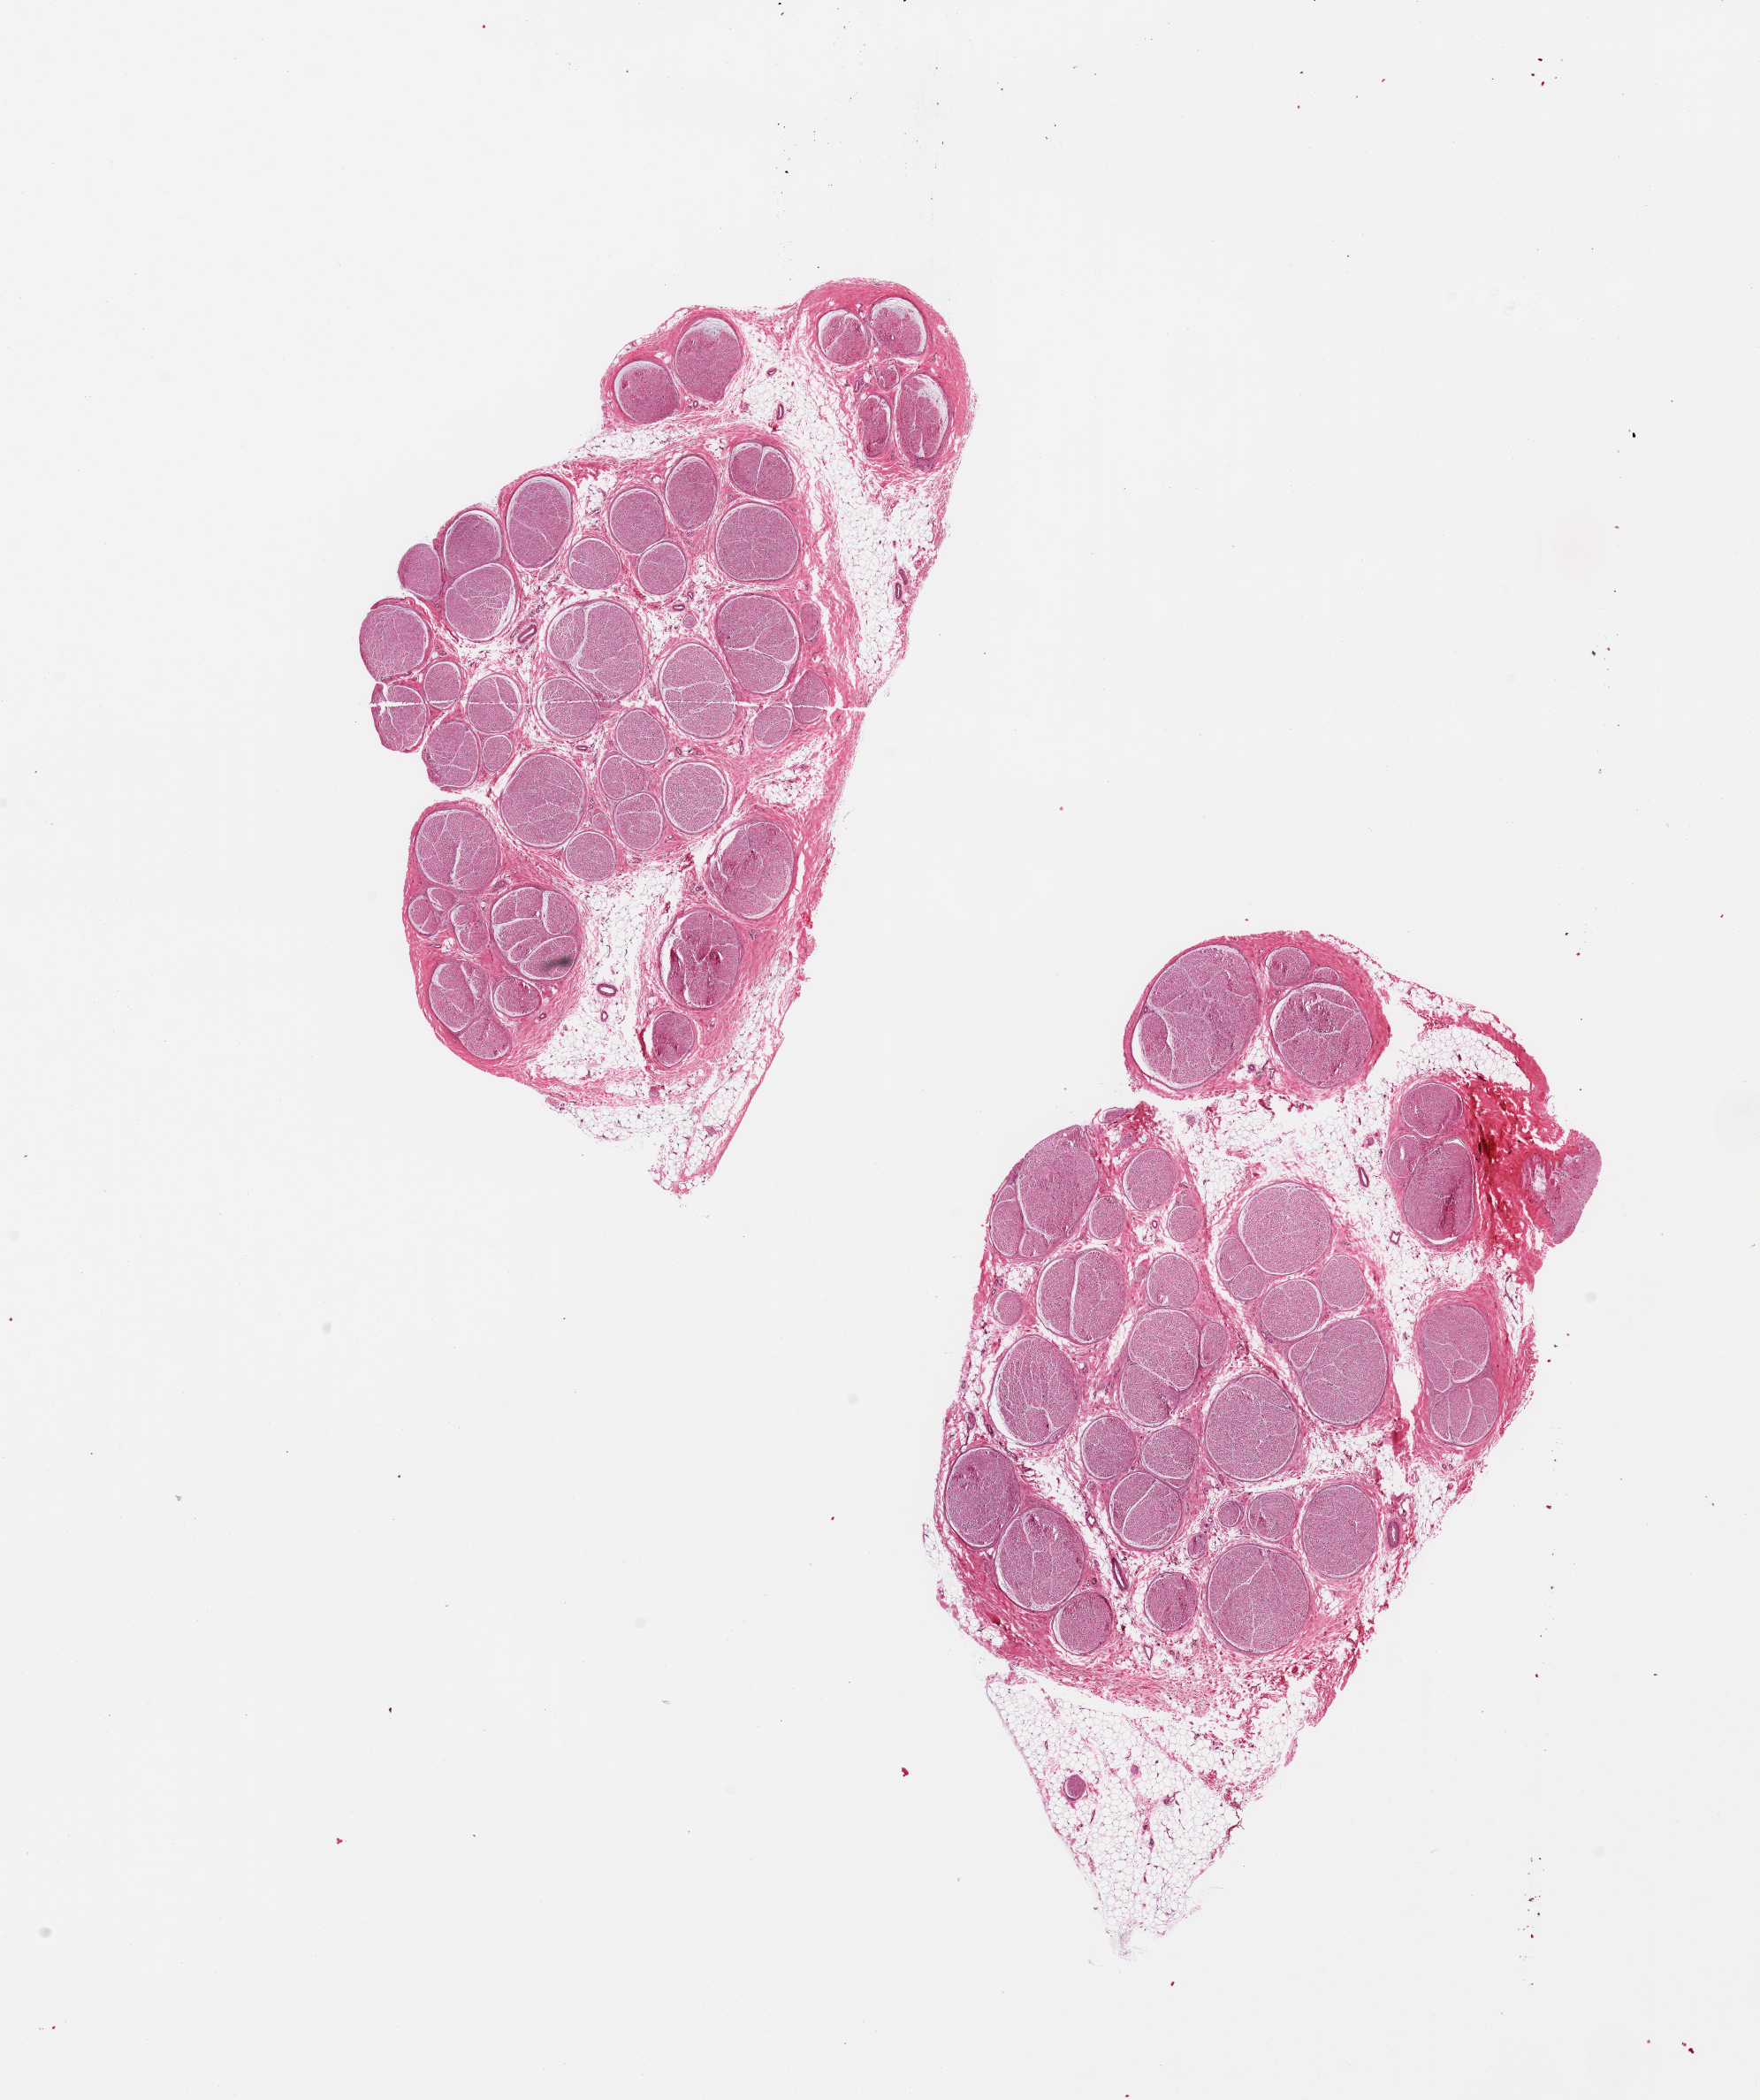
Digitized hematoxylin and eosin (H&E)-stained section, brightfield, low-resolution overview of the scanned area, about 15.8 x 18.8 mm (slide scanned at 20x); PAXgene-fixed paraffin-embedded (PFPE) section; target tissue: tibial nerve; donor tissue sample.
Review note (as recorded): 2 pieces, 2 mm nubbin adherent fat, otherwise clean.